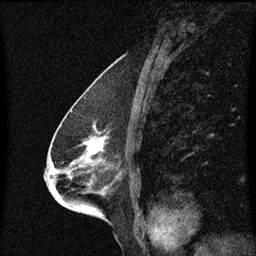
Breast MRI (dynamic contrast-enhanced), one sagittal slice; slice 34 of 60 in the series (ordered by position); dynamic contrast-enhanced series, image 2 of 3 at this slice position (ordered by acquisition); 1.5 T; TE 4.2 ms, TR 8.4 ms; 256 × 256 image matrix. Female patient, age 68 years. From the clinical record (not read from this slice): setting: breast cancer imaged before/during neoadjuvant chemotherapy; receptor status: triple-negative.
Outlined on this slice (semi-automatically segmented with operator editing):
- analysis volume of interest (the breast-tissue region the enhancement analysis was run in; not a lesion): bounding box (x1, y1, x2, y2) in pixels: (42, 114, 132, 203)
- tumour enhancement mask (voxels above the 70 % enhancement threshold inside the analysis volume of interest): (50, 138, 105, 175)